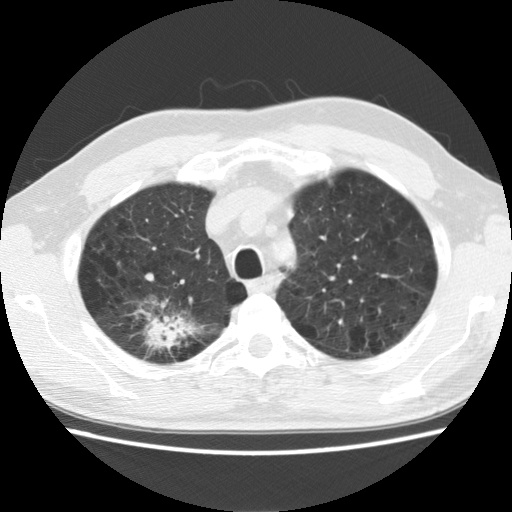
Chest CT (low-dose screening protocol), one axial image, baseline annual screen, lung window (W 1500 / L -600 HU), 2.5 mm slice thickness, slice 34 of 142 in the series. Male, age 64 years at enrolment. Former smoker at enrolment.
- Expert-annotated lung lesion, bounding box (x1, y1, x2, y2) in pixels: (114, 294, 203, 366).
- The exam's reader record, not a measurement of the box and not confirmed to be the same lesion: non-calcified nodule or mass ≥4 mm, right upper lobe, 39 × 31 mm, spiculated (stellate) margins, mixed attenuation.
- Official screen result: positive, change unspecified: nodule(s) >= 4 mm or enlarging nodule(s), mass(es), or other non-specific abnormalities suspicious for lung cancer.
- Lung cancer was diagnosed 74 days after this screen: adenocarcinoma, NOS, right upper lobe, moderately differentiated (G2), stage IB (AJCC 6th edition), 40 mm at pathology.